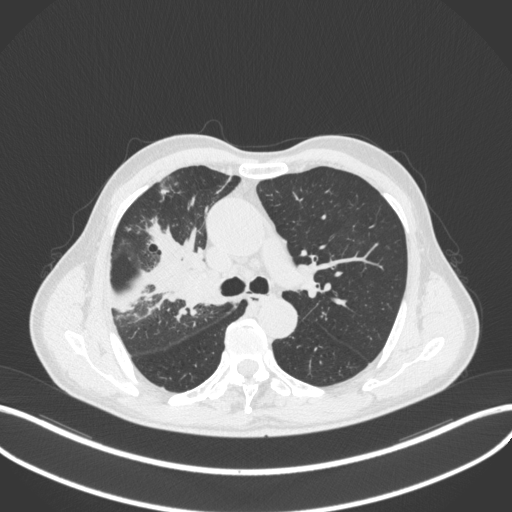
Chest CT, one axial slice; slice 319 of 490 in the series (ordered by position); 120 kVp; lung window (W 1500 / L -600 HU); 1 mm slice thickness; 512 × 512 image matrix, field of view 400 × 400 mm. Male patient, age 69 years. From the clinical record (not read from this slice): clinical TNM (as recorded): T2a N0 M0.
Annotated regions visible in this slice (rectangle marked by the reading radiologist):
- lung tumour (recorded histology: adenocarcinoma): bounding box (x1, y1, x2, y2) in pixels: (172, 266, 219, 309)